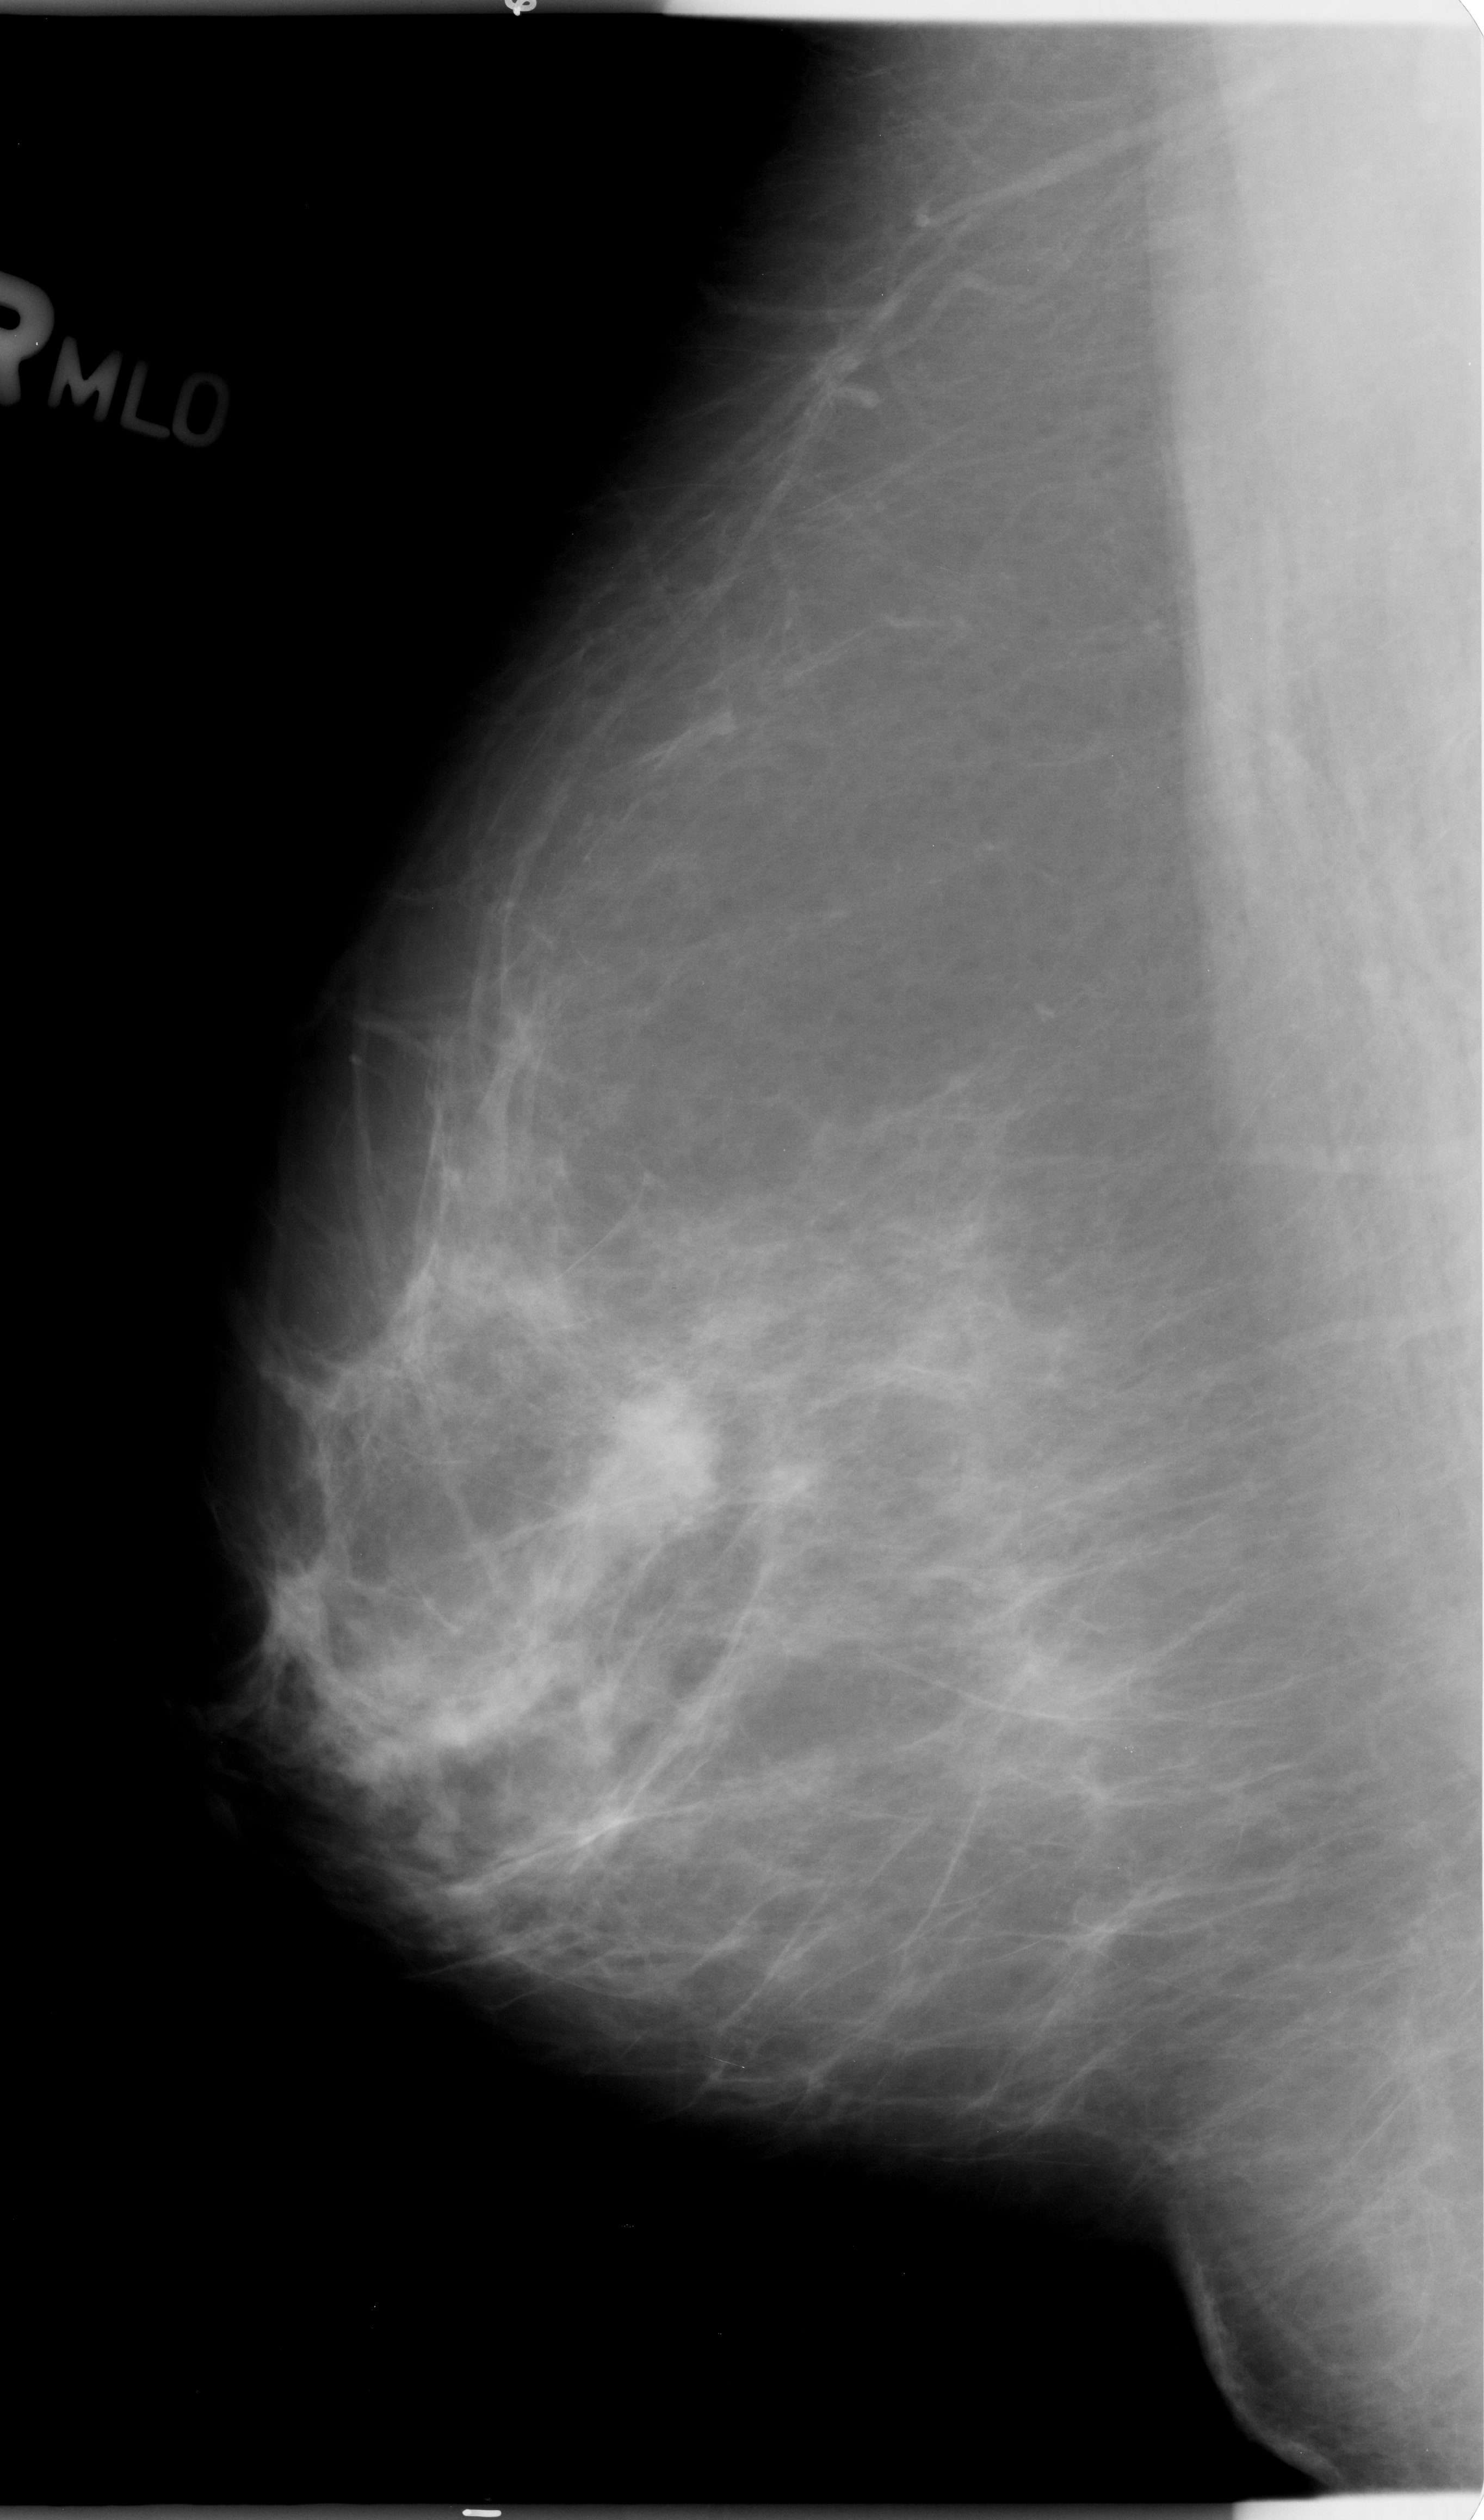
Scanned film-screen mammogram; right breast; mediolateral oblique (MLO) view; BI-RADS breast density category 2 (scale 1–4); 1484 × 2520 image matrix.
Expert-marked regions of interest on this film, with their recorded descriptors:
- mass, shape irregular, margins microlobulated / ill defined; BI-RADS assessment category 4; subtlety rating 4 on a 1 (subtle) to 5 (obvious) scale; pathology result (as recorded, not read from the image): malignant: bounding box [x1, y1, x2, y2] px = [578, 1398, 726, 1564]